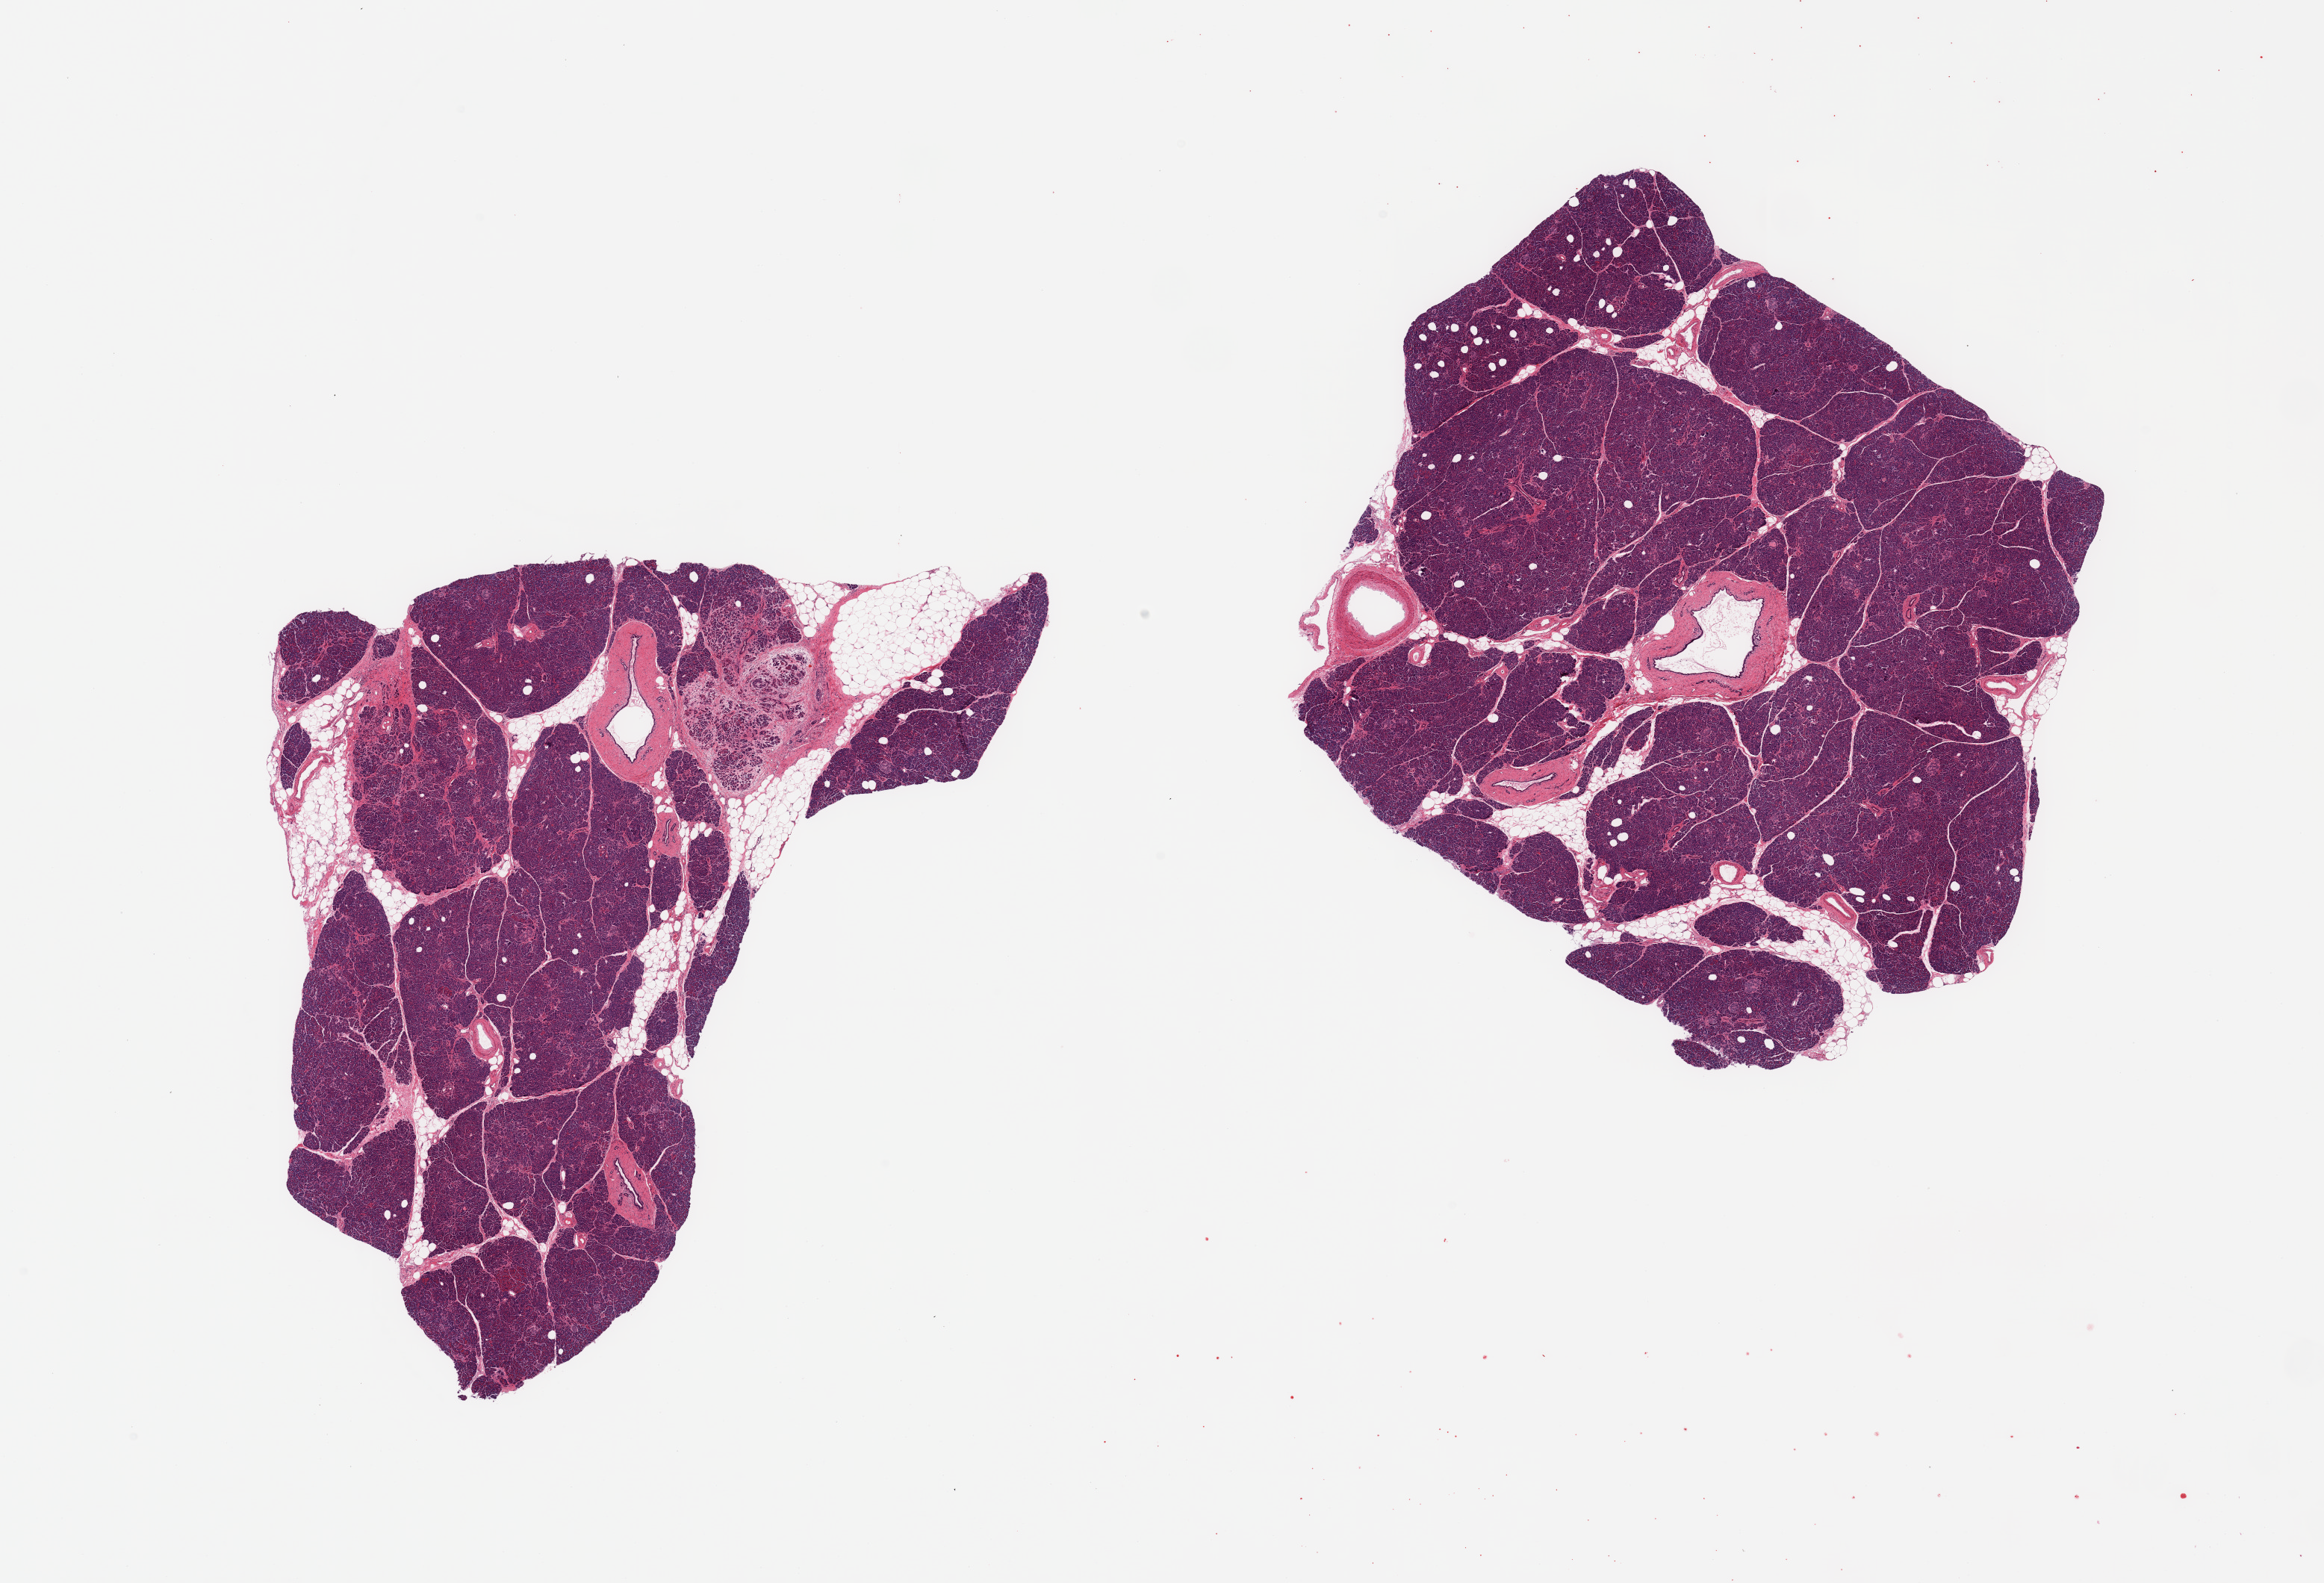
Digitized hematoxylin and eosin (H&E)-stained section, brightfield, a low-resolution overview of the entire scanned area, about 24.6 x 16.8 mm; PAXgene-fixed, paraffin-embedded tissue; sampled site (target tissue): pancreas; donor tissue sample. Donor: female.
Pathologist's review note for this sample: 2 pieces, focal remote pancreatitis; Islets well preserved; encirlced.